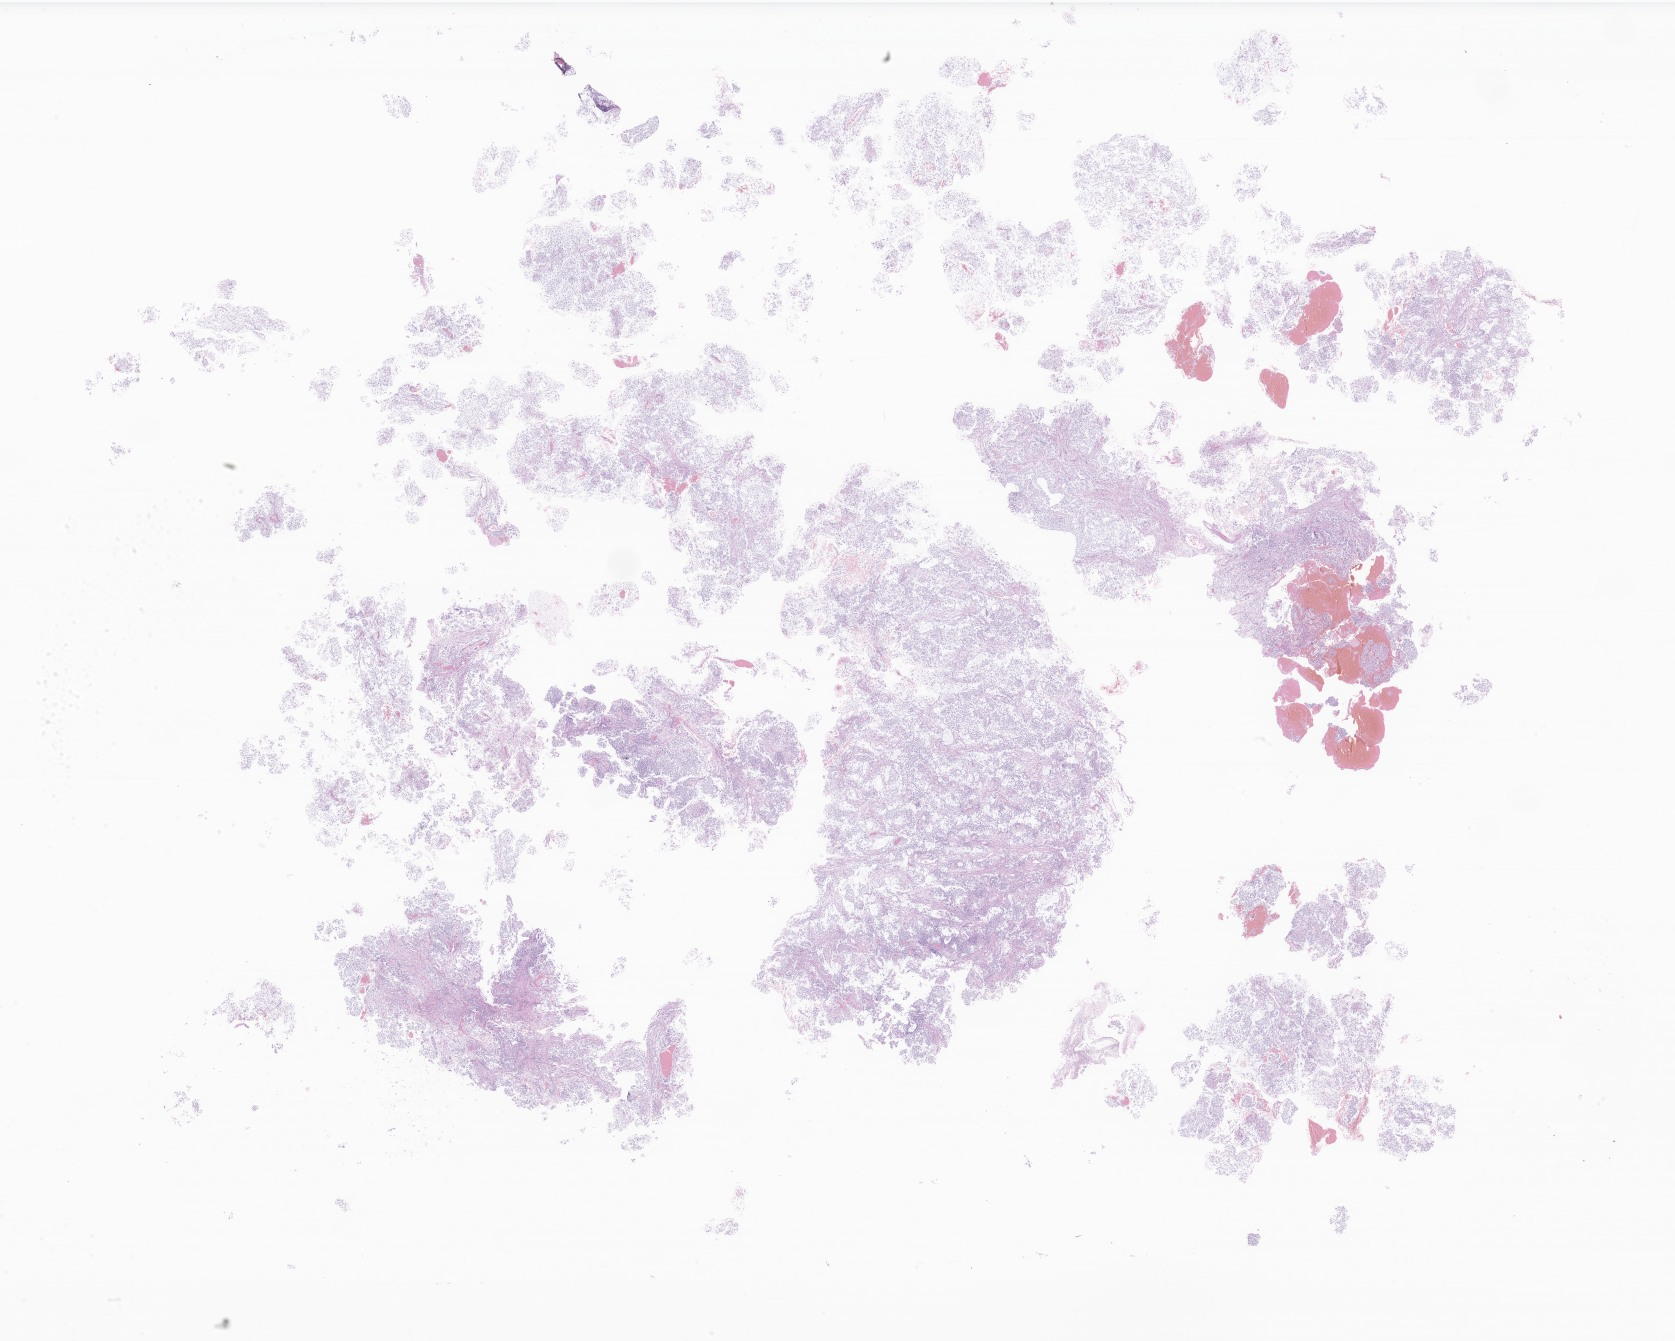
Digitized H&E-stained section of tumor tissue from the frontal lobe — low-resolution overview of the scanned area, about 28.3 x 22.6 mm, formalin-fixed, paraffin-embedded (FFPE) tissue. Patient: male, age 163 days.
Diagnosis: Neoplasm, metastatic.